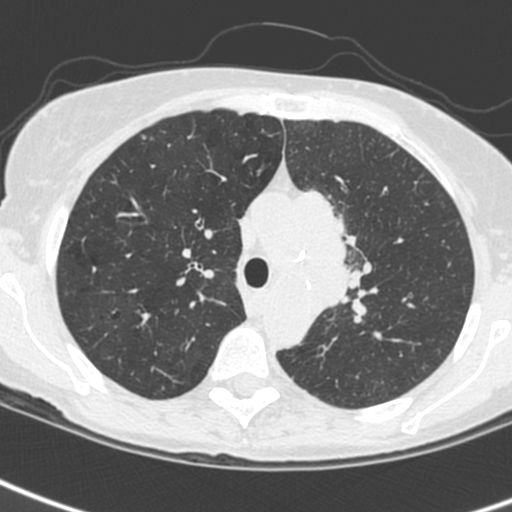
Low-dose screening chest CT, one axial slice. Position 178 of 242 along the scan axis. 120 kVp. Lung window (W 1500 / L -600 HU). 1.3 mm slice thickness. 512 × 512 image matrix, field of view 284 × 284 mm.
Annotated regions visible in this slice (outlined manually by an expert reader):
- lesion 3 (tumor, upper lobe of left lung): box from (x=300, y=190) to (x=351, y=314) px